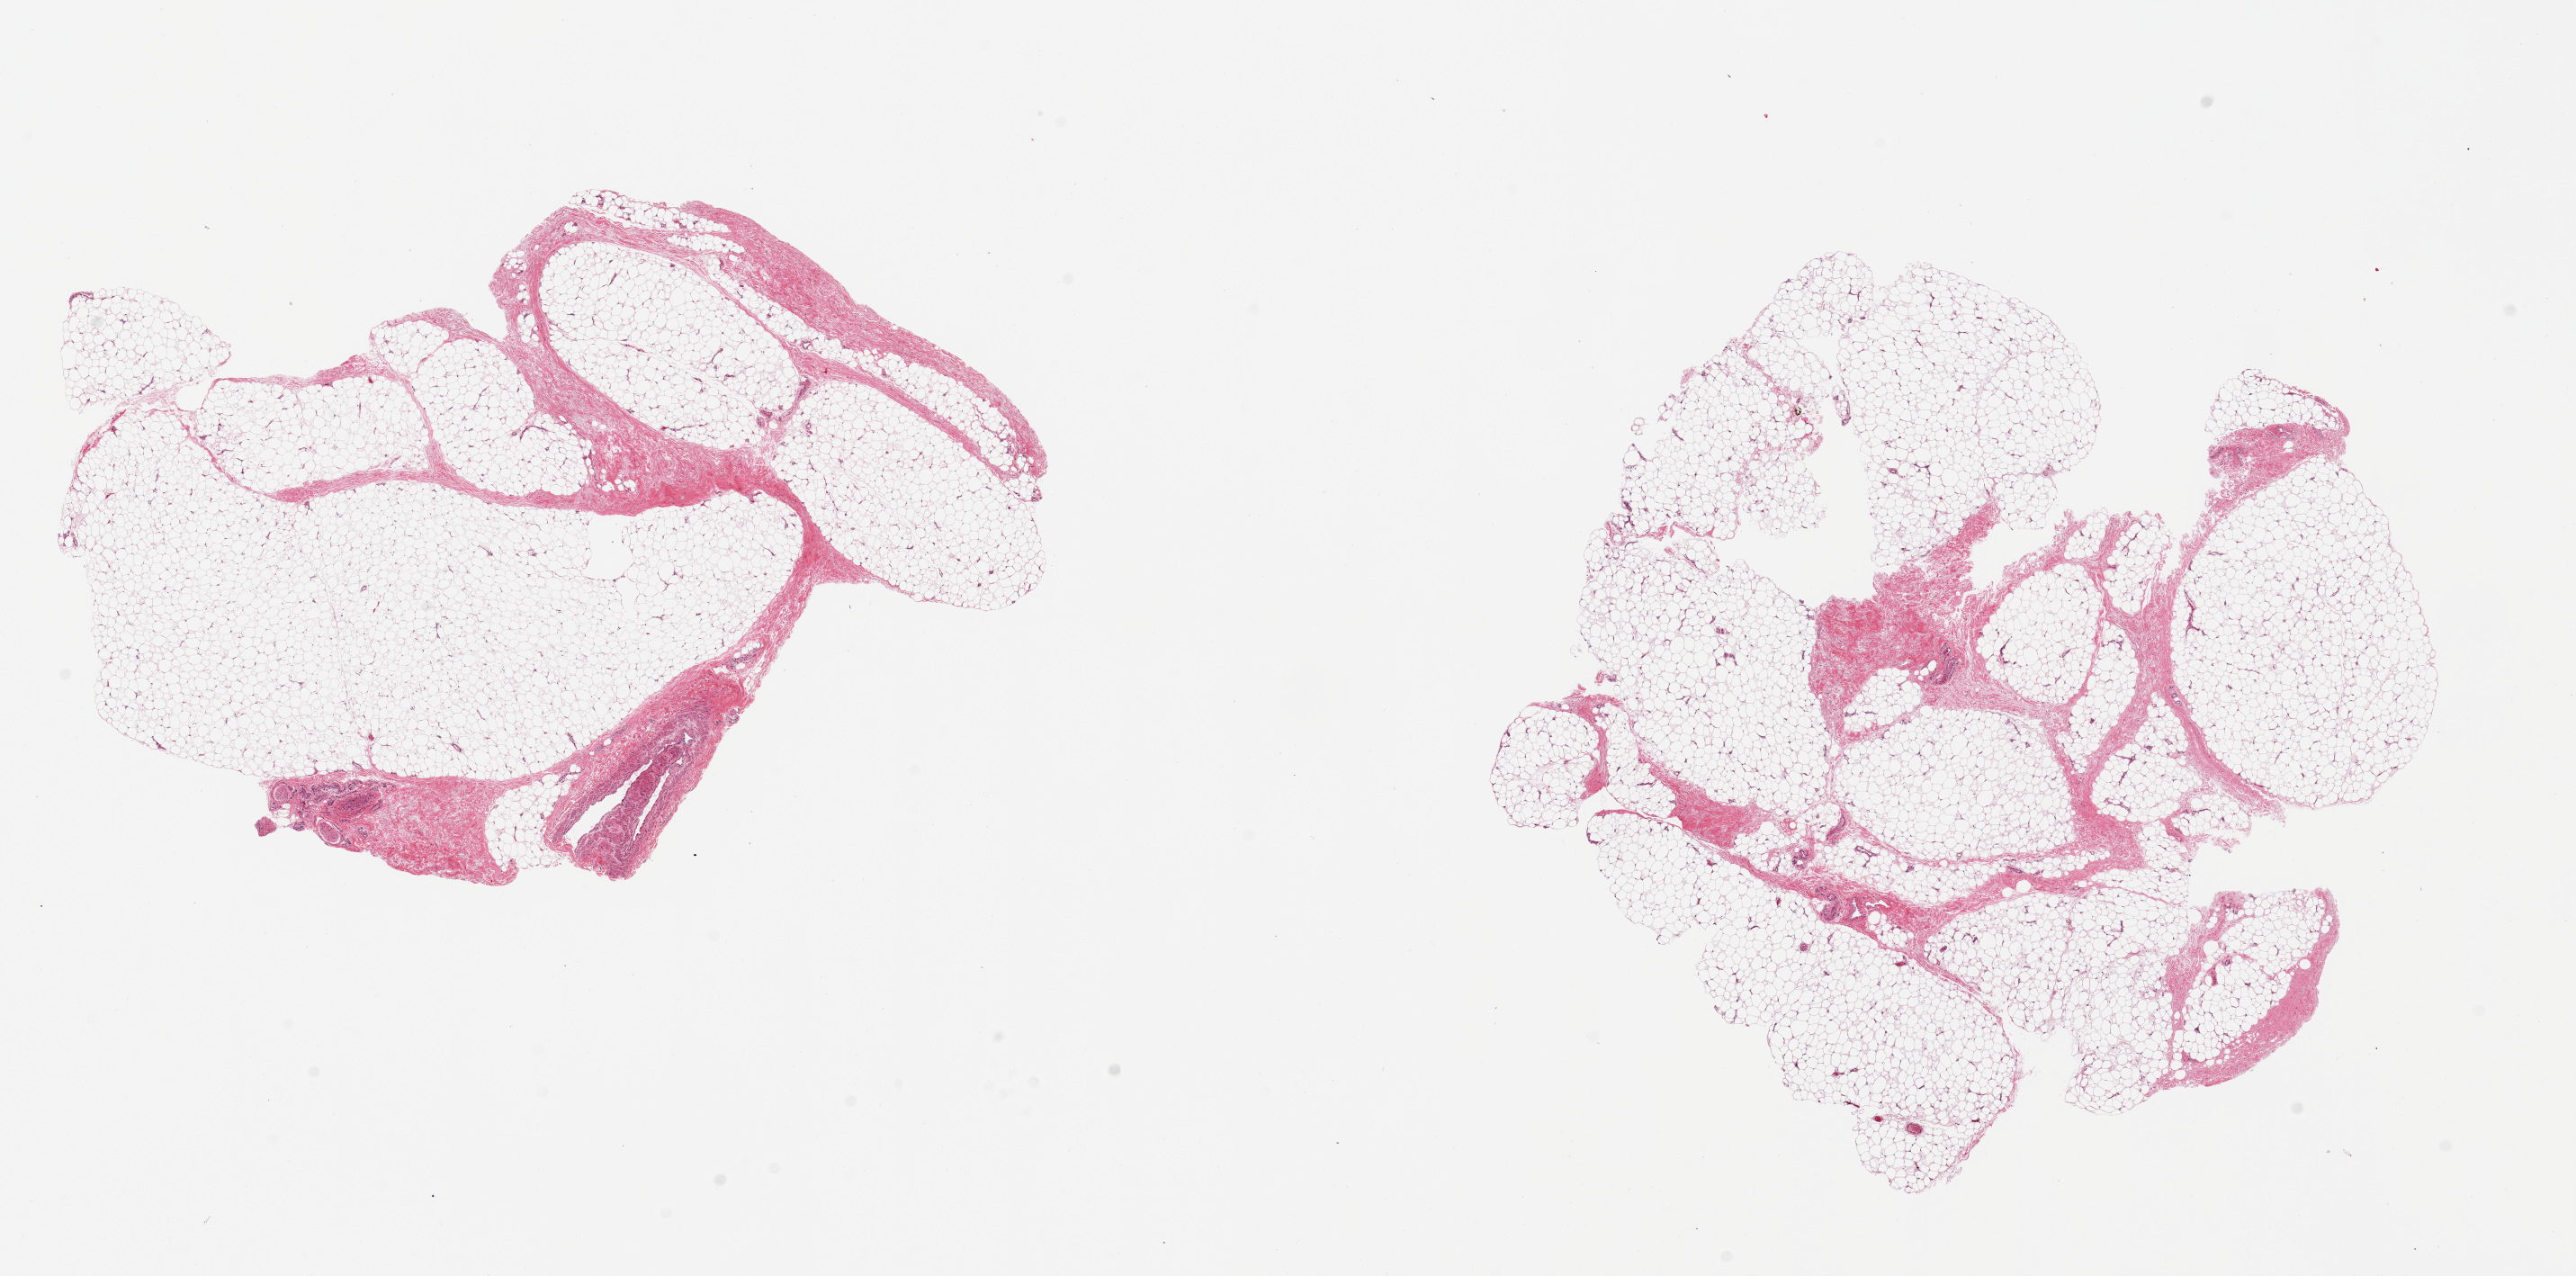
Whole-slide image, hematoxylin and eosin (H&E) stain — low-resolution overview of the scanned area, about 22.6 x 11.2 mm (slide scanned at 20x); PAXgene-fixed, paraffin-embedded tissue; sampled site (target tissue): adipose tissue; donor tissue sample. Male donor.
Review note (as recorded): 2 pieces; 10 - 15% fibrovascular component and nerves.